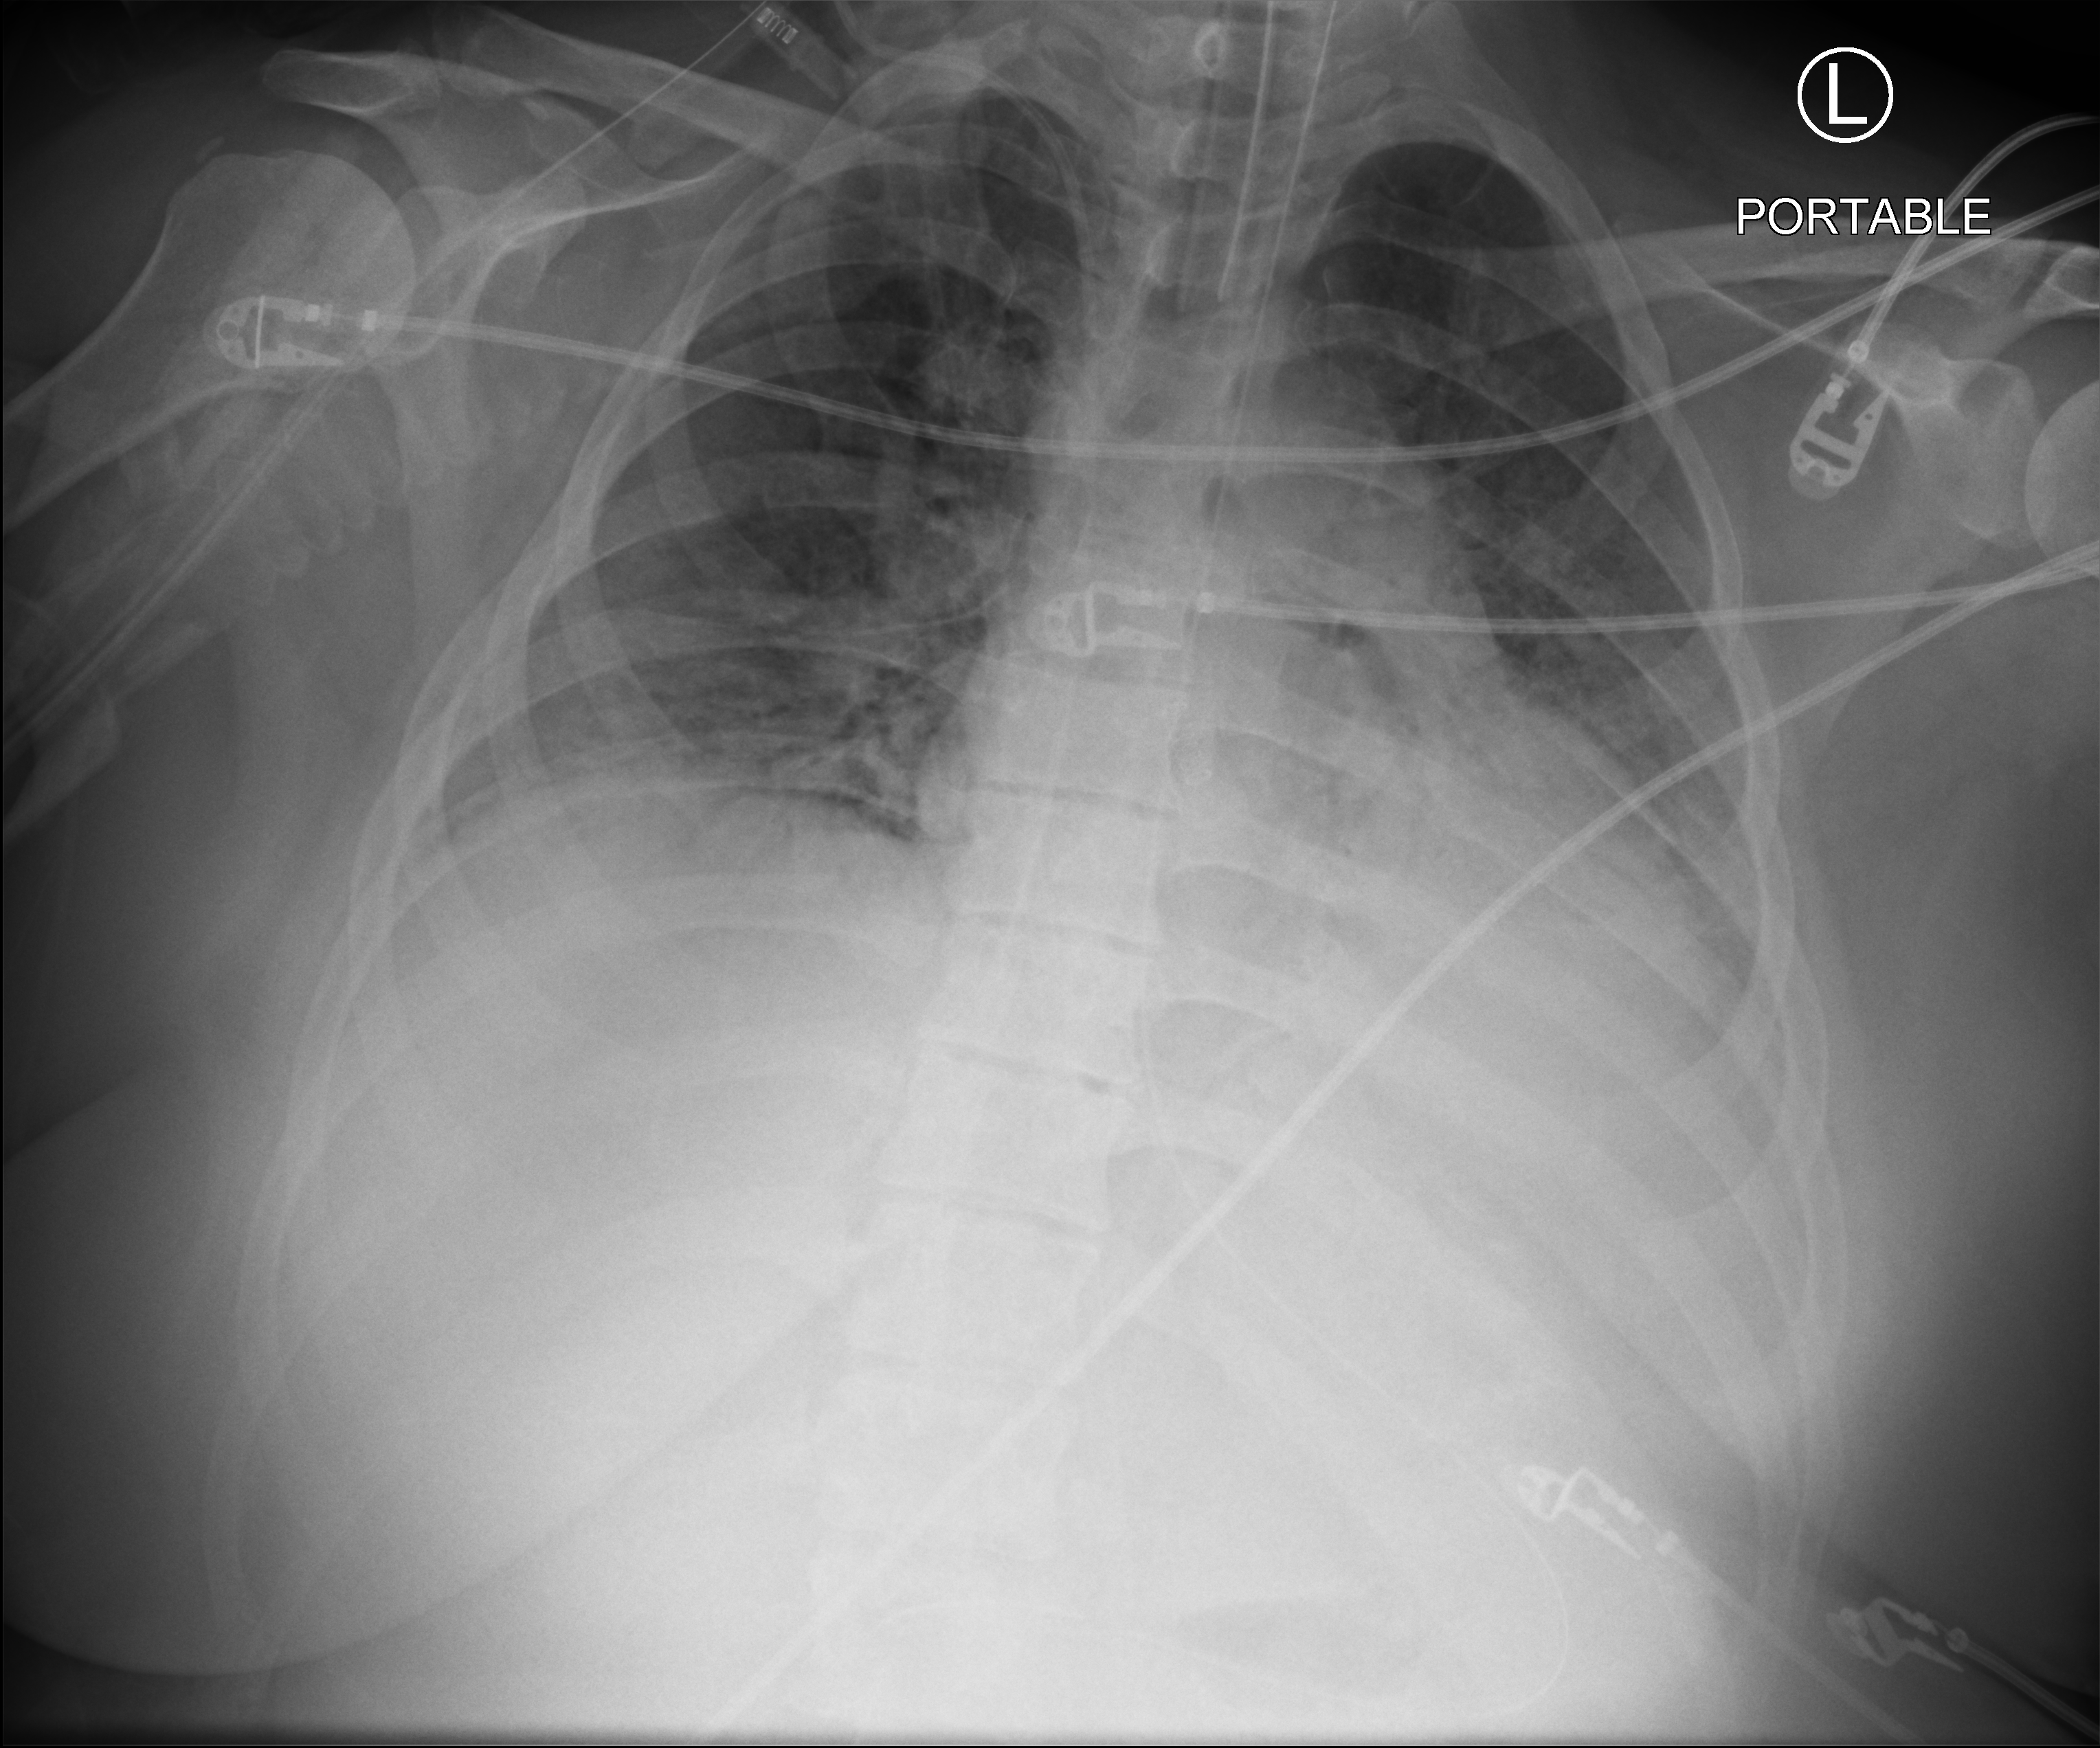
Portable chest radiograph; anteroposterior (AP) projection. Patient hospitalised with COVID-19; female, aged 18–59 years.
From the hospital-stay record, not from the radiograph (when in the stay this image was taken is not recorded): admitted to intensive care during this hospital stay: yes; mechanically ventilated during this hospital stay: yes; chronic kidney disease (admission record): no.